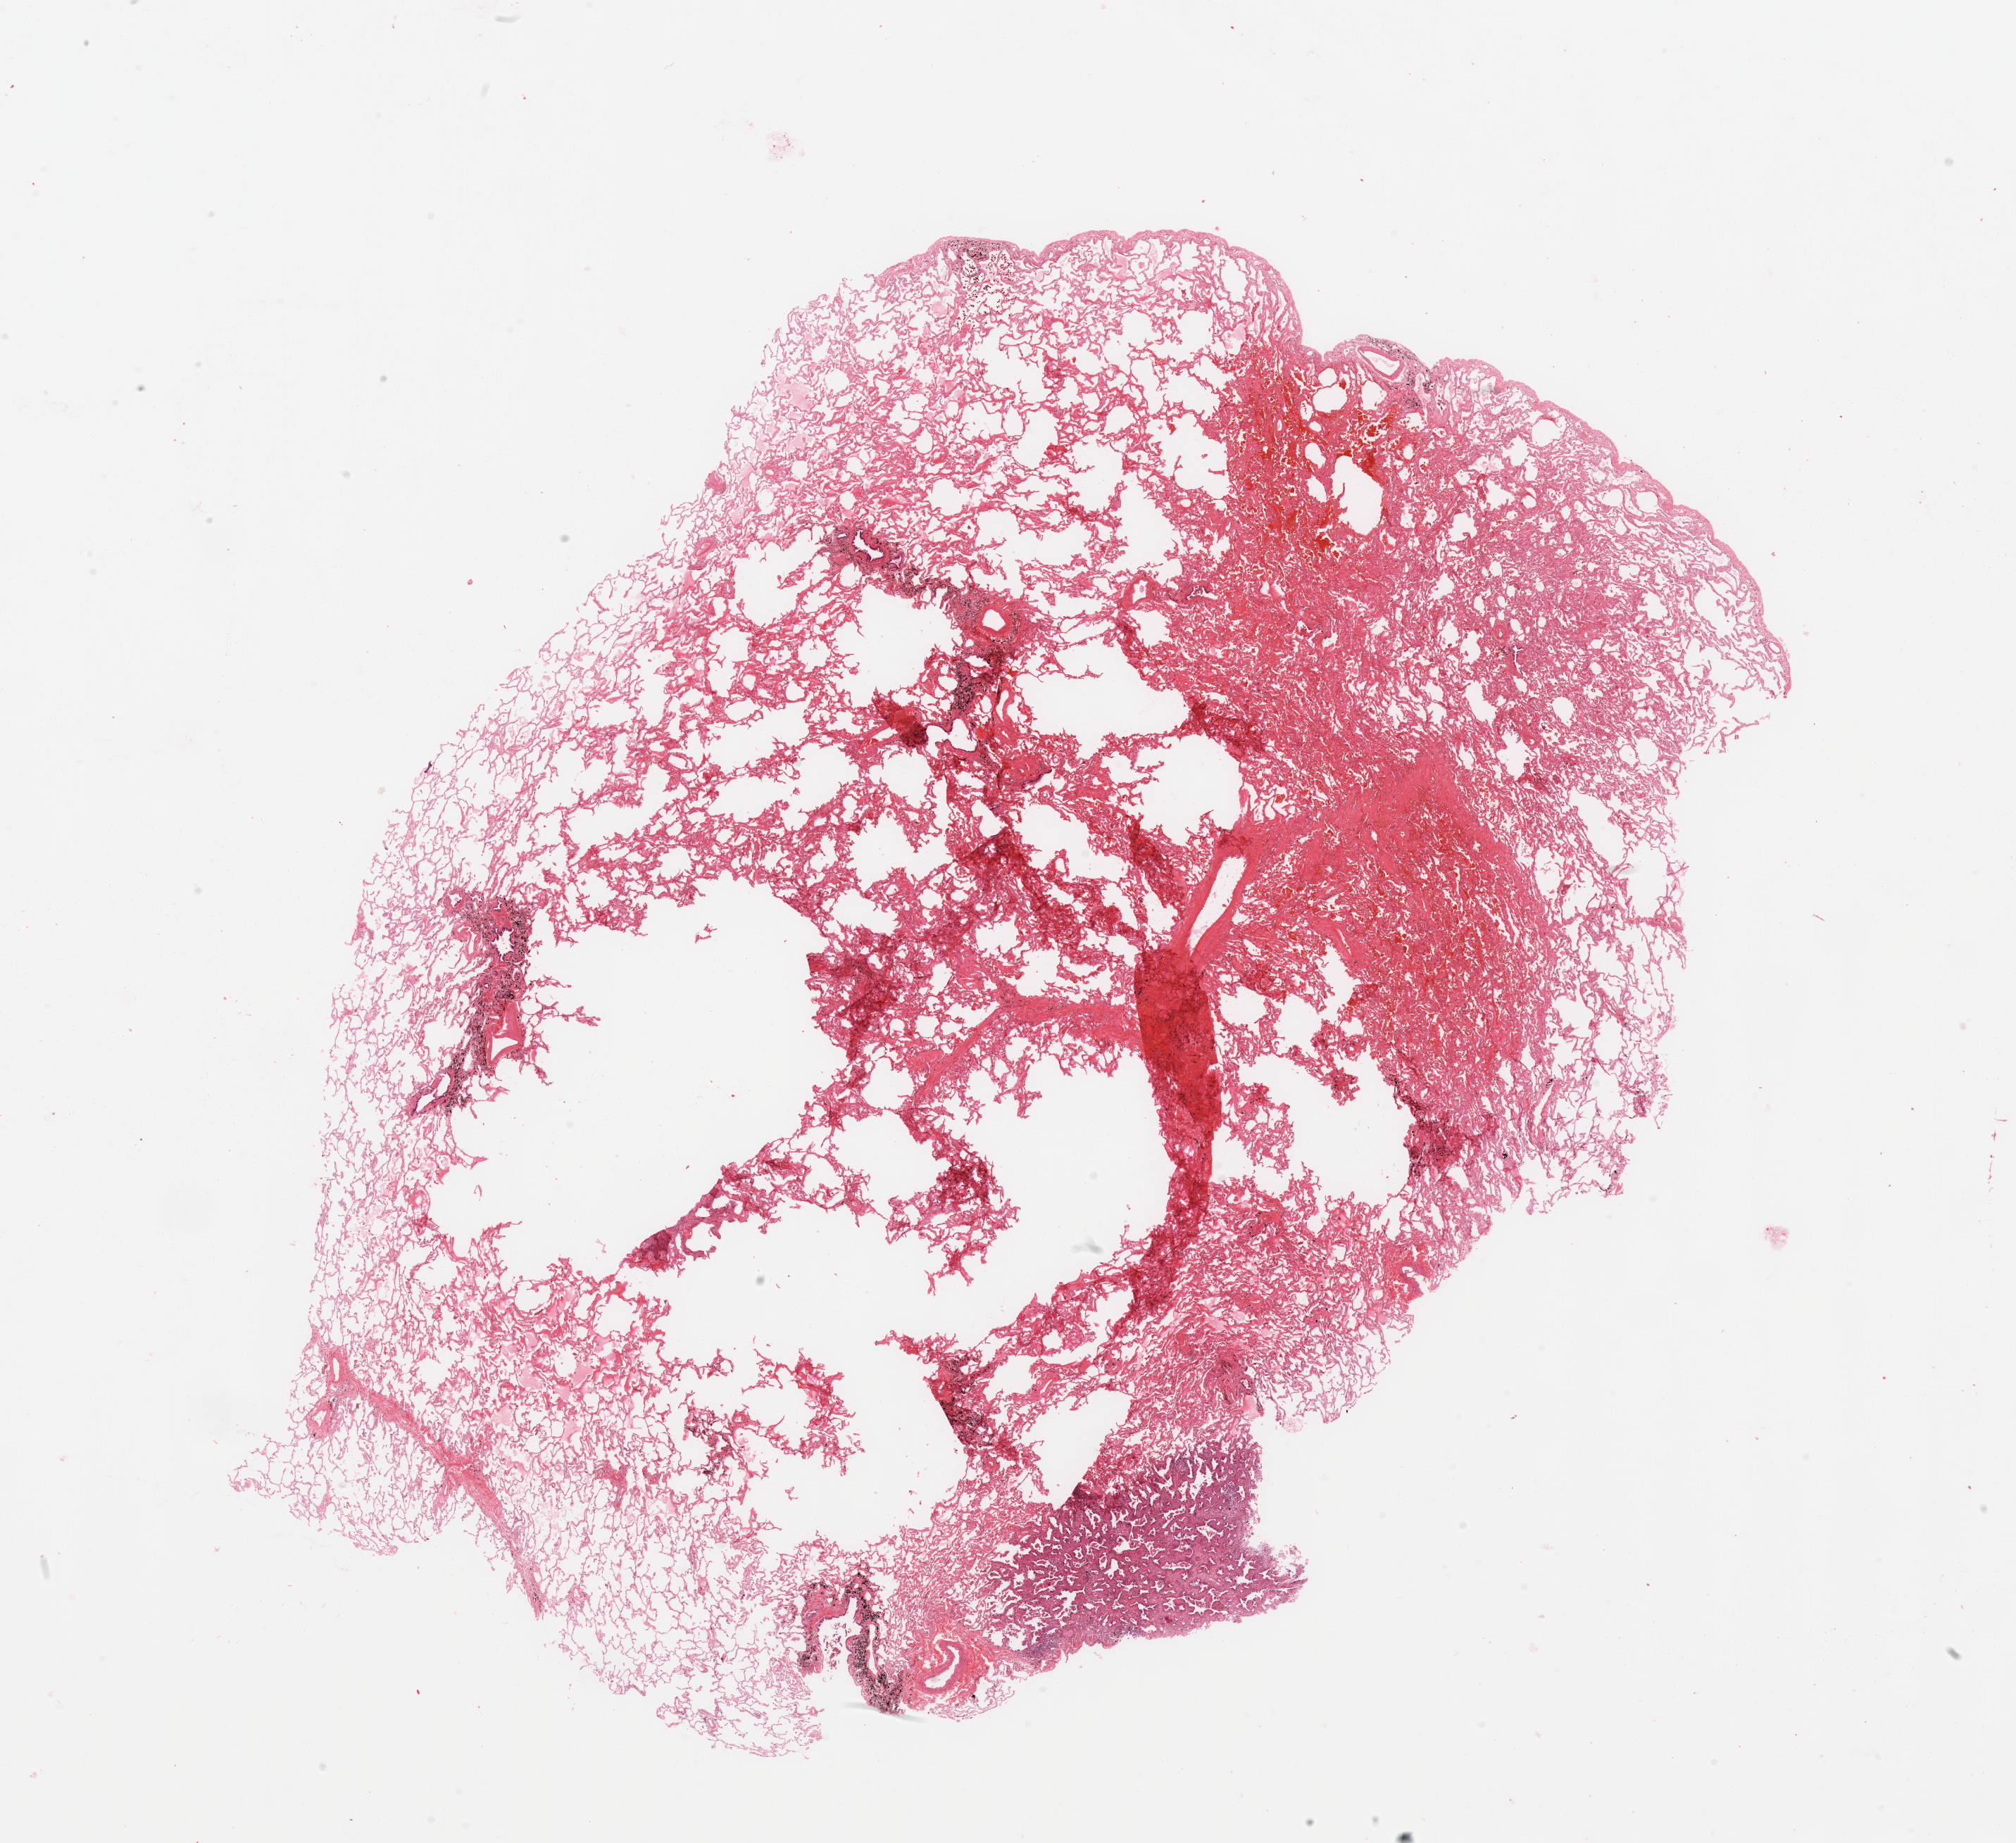
Digitized Hematoxylin and eosin (H&E) stained tissue section (whole slide) — a low-resolution overview of the entire scanned area, about 22.6 x 20.7 mm. Normal (non-tumour) tissue sample, lung. Female, 67 y/o.
This section: normal (non-tumour) tissue from the same patient. Patient diagnosis: Adenocarcinoma, NOS.